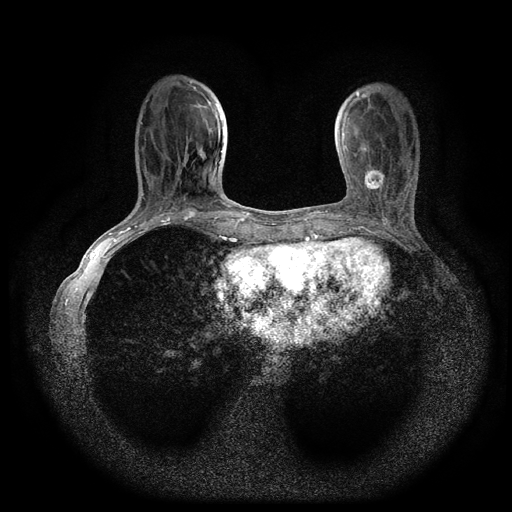
Breast MRI (dynamic contrast-enhanced, multi-phase), one axial slice. Slice 31 of 116 in the series (ordered by position). Dynamic contrast-enhanced series, time point 2 of 5 at this slice position (early post-contrast). 1.5 T. TE 2.7 ms, TR 5.4 ms. 512 × 512 image matrix, field of view 330 × 330 mm. Patient: female, 49 years.
Structures marked on this image (semi-automatically segmented with operator editing):
- breast lesion (labelled 'tumour' in the annotation; benign lesions carry a separate 'benign' label): bounding box <362,167,386,194> (left, top, right, bottom; pixels)